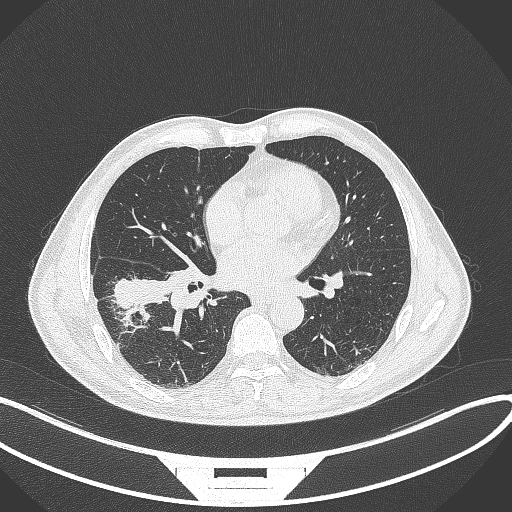
Chest CT, one axial slice; position 167 of 364 along the scan axis; reconstruction kernel B70f; 120 kVp; lung window (W 1500 / L -600 HU); 1 mm slice thickness; 512 × 512 image matrix, field of view 400 × 400 mm. Male patient, age 58 years. From the clinical record (not read from this slice): clinical TNM (as recorded): T3 N0 M0.
Structures marked on this image (rectangle marked by the reading radiologist):
- lung tumour (recorded histology: squamous cell carcinoma): bounding box (x1, y1, x2, y2) in pixels: (109, 271, 168, 314)